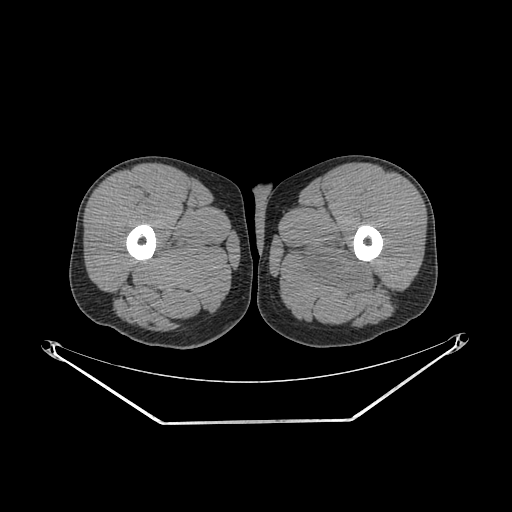
CT of an extremity soft-tissue mass (from a PET/CT study), one axial slice; position 248 of 267 along the scan axis; reconstruction kernel SOFT; soft-tissue window (W 400 / L 40 HU); 512 × 512 image matrix, field of view 500 × 500 mm. Male patient. From the clinical record (not read from this slice): histological type: extraskeletal osteosarcoma; grade: high; site of the primary tumour: left adductur.
Structures marked on this image (expert contour drawn on MRI and transferred to this co-registered scan by the dataset authors):
- gross tumour volume (mass): bounding box (x1, y1, x2, y2) in pixels: (290, 231, 378, 295)